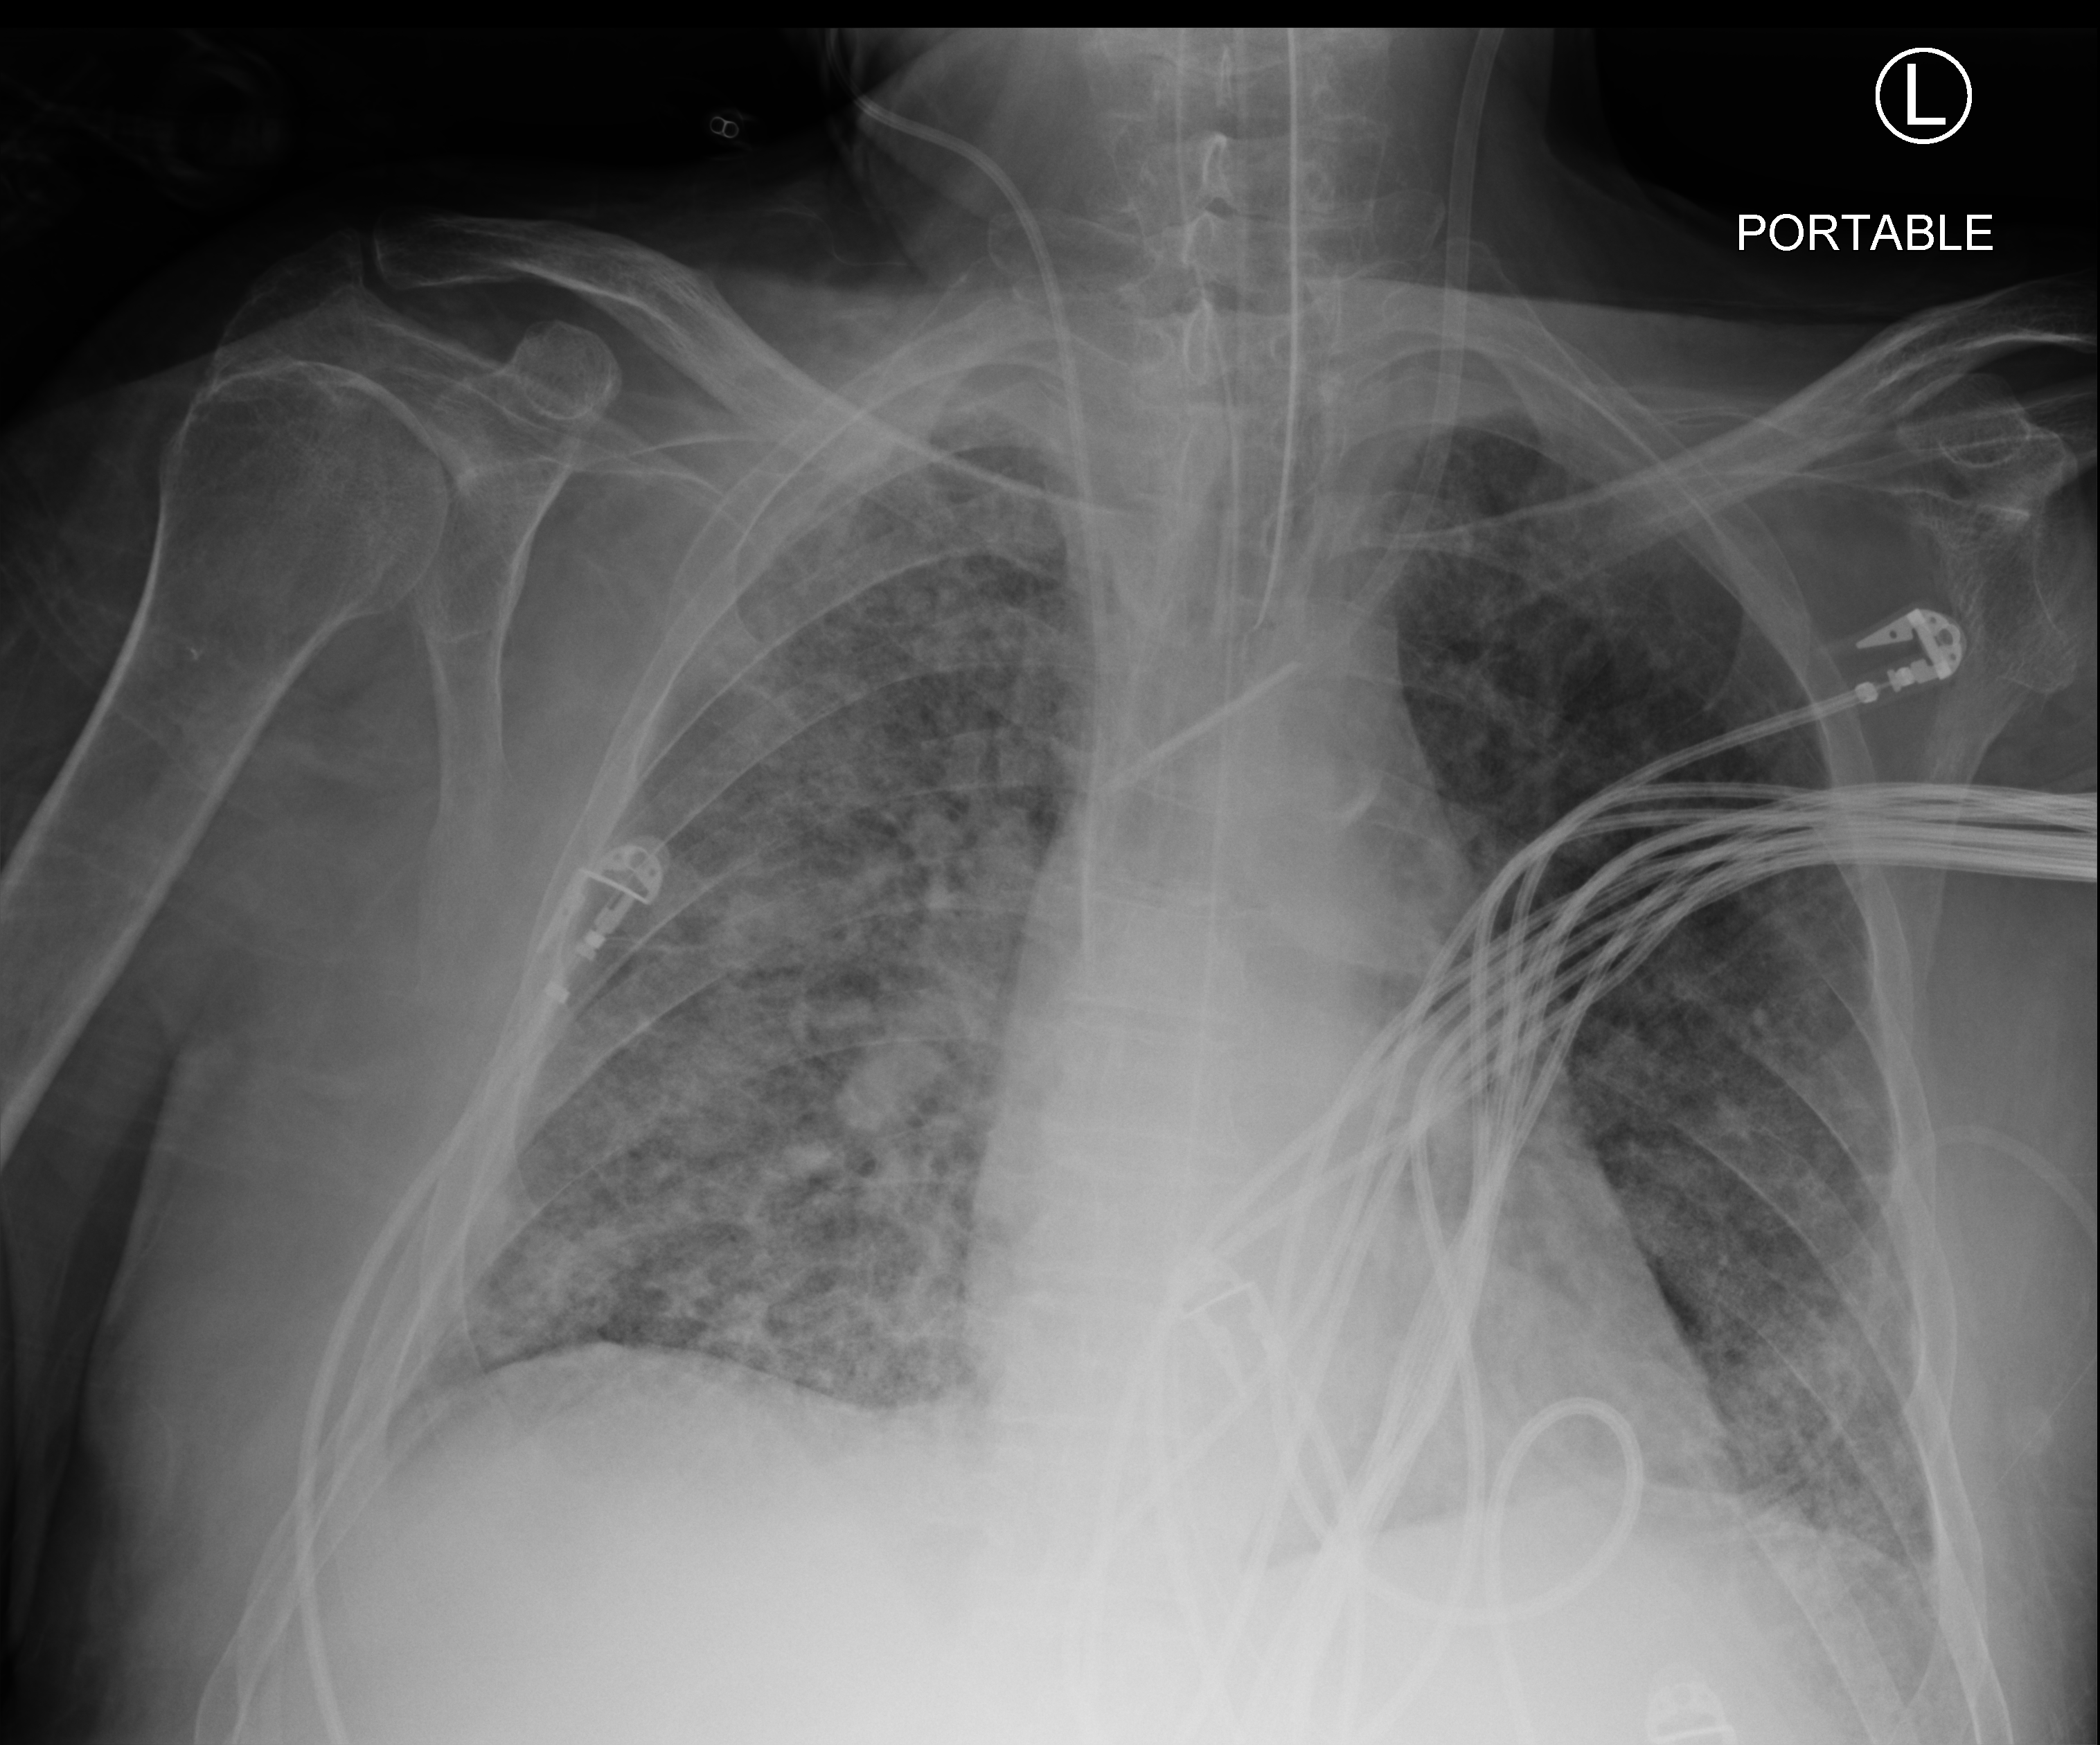
Chest X-ray (portable); anteroposterior (AP) projection. Patient hospitalised with COVID-19; male, aged 60–74 years.
Hospital-stay facts (about this admission, not read from this image; timing relative to this image not recorded): other chronic lung disease (admission record): no.